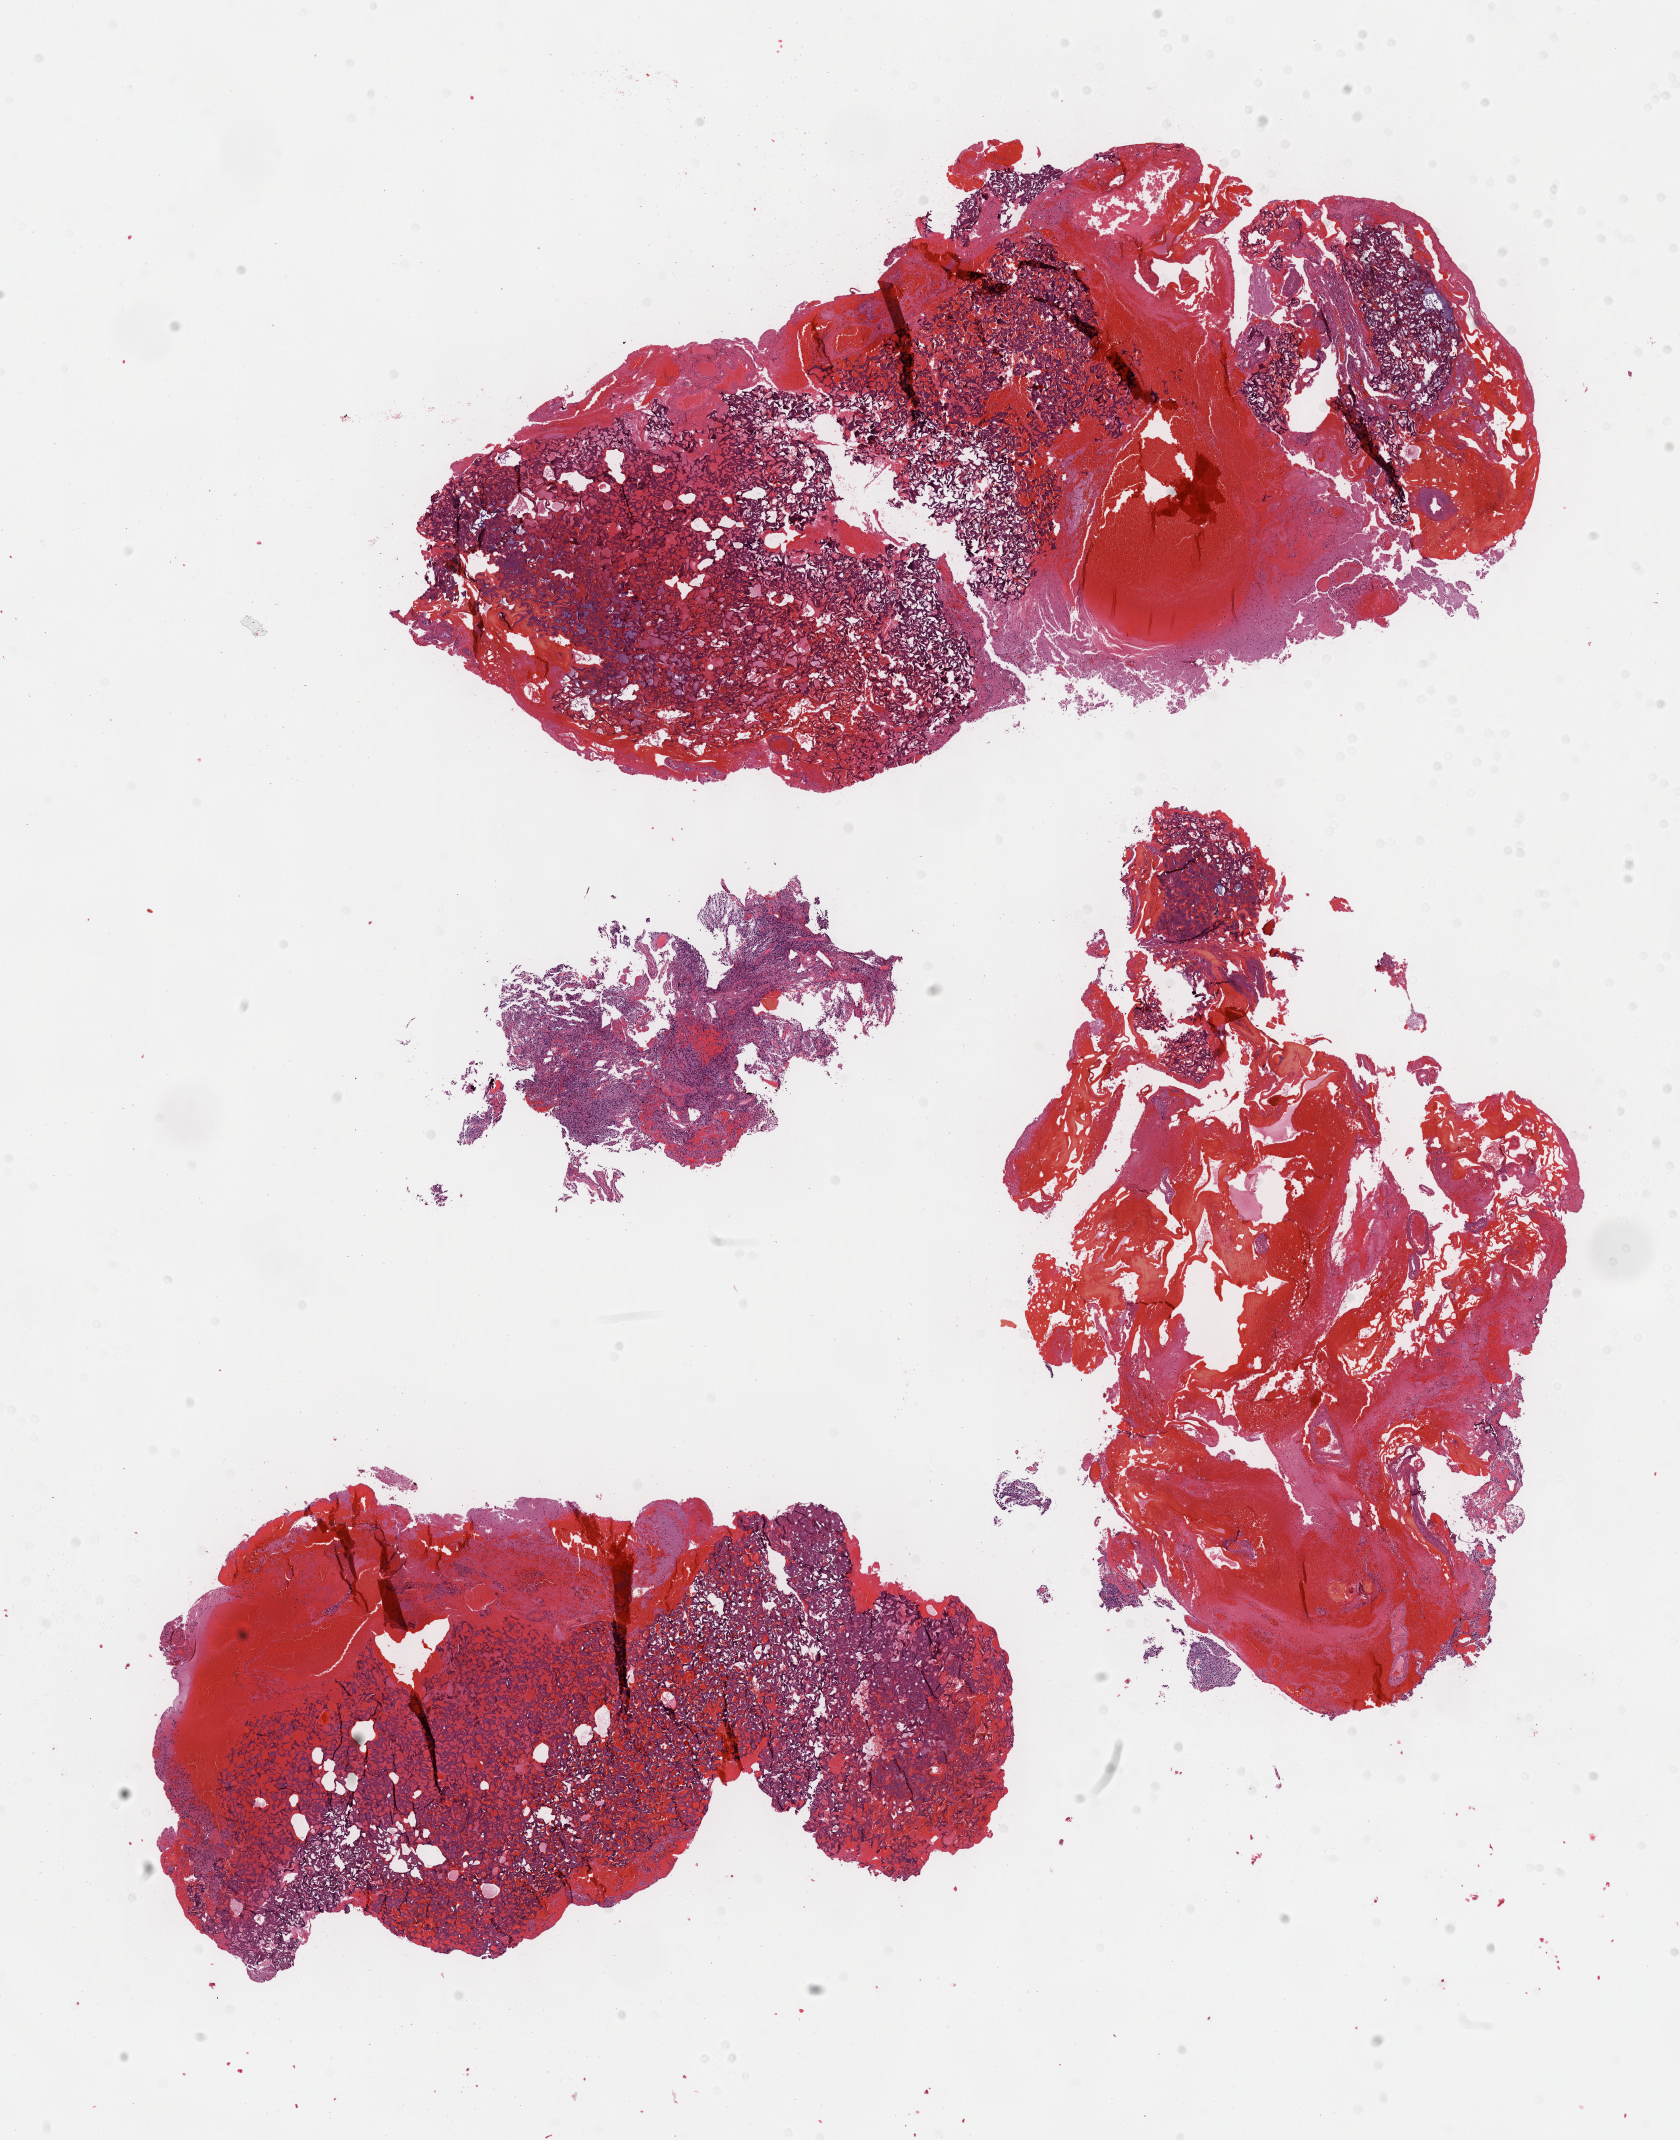
H&E whole-slide image, whole scanned area (about 13.6 x 17.3 mm) shown as a low-resolution overview, FFPE section, brain, primary tumour sample. Patient: male, age at initial diagnosis 26 years. Histologic grade: G2 (moderately differentiated).
Laterality: left. Histologic diagnosis: Astrocytoma, NOS (cerebrum).